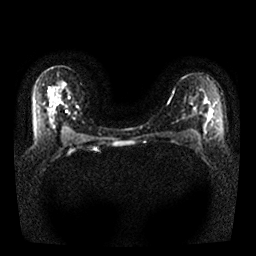
Breast MRI, one axial slice. Position 17 of 25 along the scan axis. Diffusion-weighted series; image 2 of 4 stored at this slice position (different b-values; order by instance number). 1.5 T. 4 mm slice thickness. 256 × 256 image matrix. Female patient.
Annotated regions visible in this slice (expert manual segmentation):
- tumour on diffusion-weighted imaging: box from (x=207, y=110) to (x=213, y=118) px